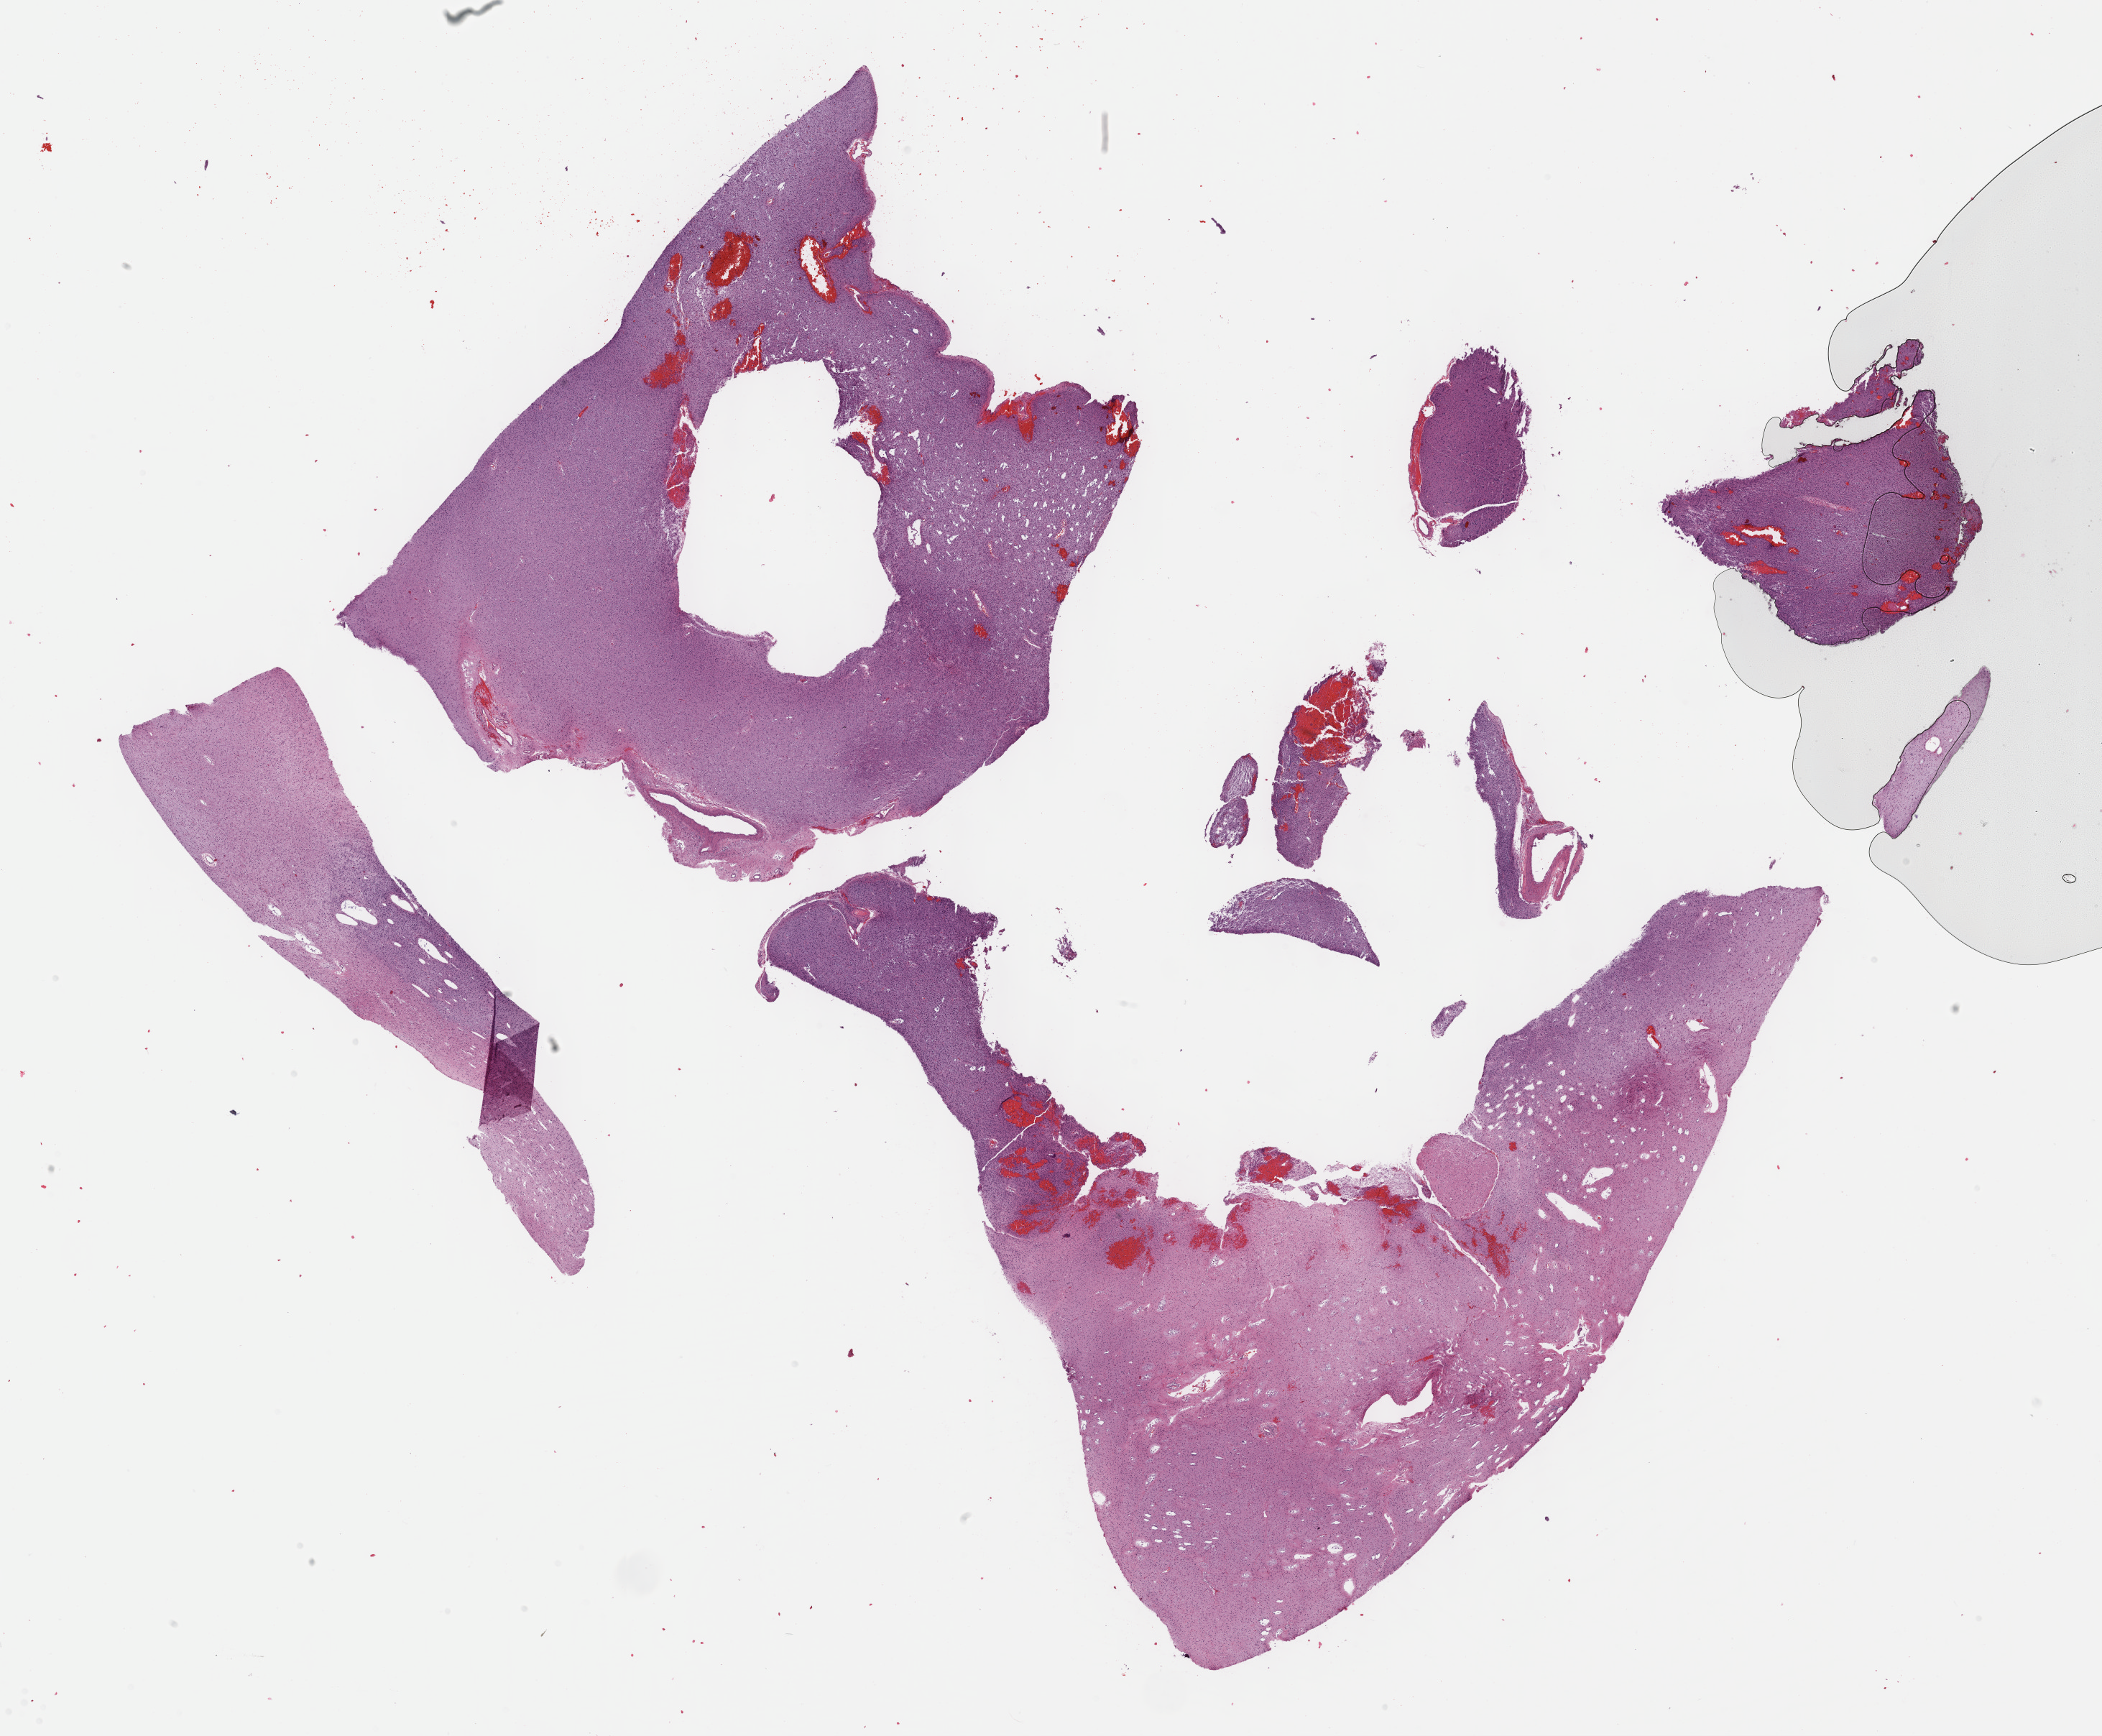
Digitized Hematoxylin and eosin (H&E) stained tissue section (whole slide), shown as a low-resolution overview of the whole scanned area (about 23.7 x 19.5 mm, acquisition: 40x scan), formalin-fixed paraffin-embedded (FFPE) diagnostic section, brain, primary tumour sample. Patient: male, age at initial diagnosis 29 years.
Histologic diagnosis: Oligodendroglioma, NOS.